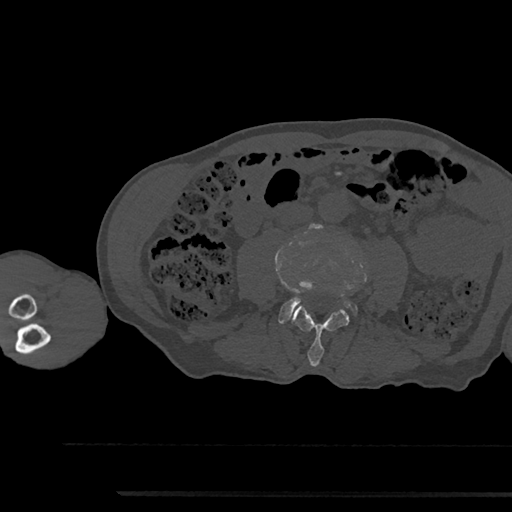
CT including the spine, one axial slice; position 453 of 797 along the scan axis; 120 kVp; bone window (W 1800 / L 400 HU); 0.5 mm slice thickness; 512 × 512 image matrix, field of view 367 × 367 mm. Male patient, age 79 years. From the clinical record (not read from this slice): primary cancer: prostate.
Outlined on this slice (semi-automatically segmented with operator editing):
- L3 vertebra: box from (x=292, y=306) to (x=349, y=366) px
- L4 vertebra: (x=279, y=282)–(x=357, y=323)